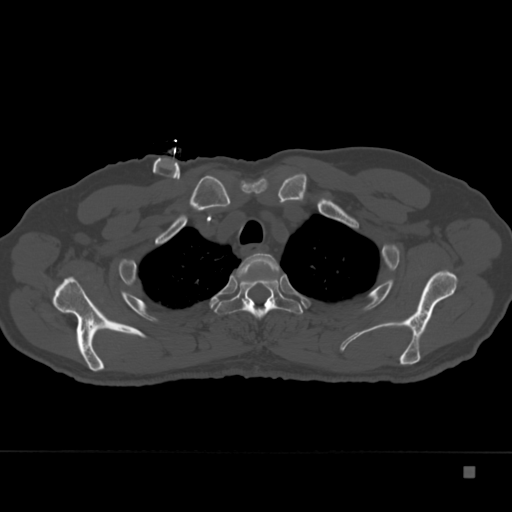
CT including the spine, one axial slice. Slice 290 of 332 in the series (ordered by position). 120 kVp. Bone window (W 1800 / L 400 HU). 512 × 512 image matrix, field of view 389 × 389 mm. Patient: male, 72 years. Case-level facts recorded for this patient, not image findings: primary cancer: skeletal.
Structures marked on this image (semi-automatic segmentation, software-assisted and operator-edited):
- T2 vertebra: bounding box <232,253,280,281> (left, top, right, bottom; pixels)
- T3 vertebra: <214,272,303,319>